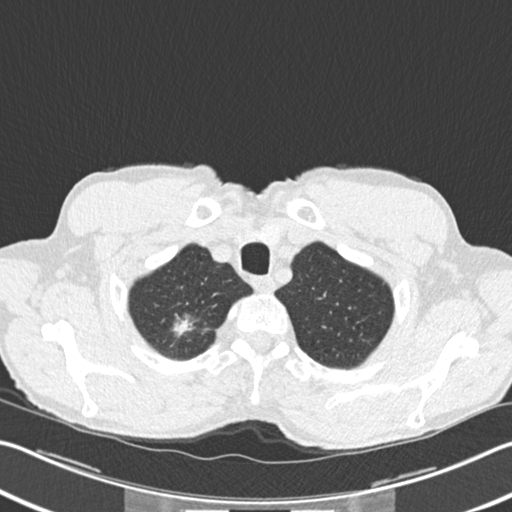
Low-dose screening chest CT, one axial slice; position 200 of 220 along the scan axis; 120 kVp; lung window (W 1500 / L -600 HU); 2 mm slice thickness; 512 × 512 image matrix, field of view 342 × 342 mm.
Outlined on this slice (expert manual segmentation):
- lesion 1 (tumor, upper lobe of right lung): box from (x=174, y=316) to (x=194, y=336) px